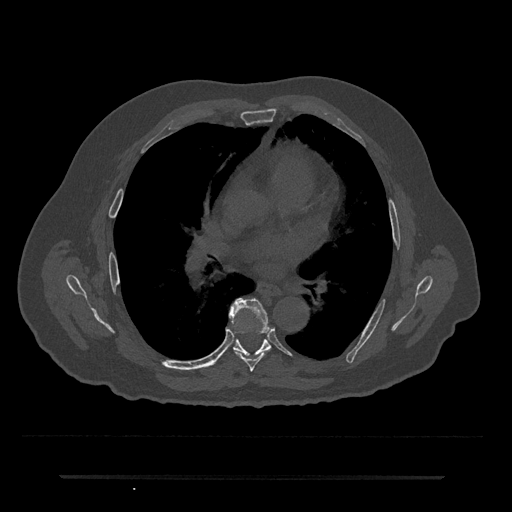
CT including the spine, one axial slice; slice 414 of 797 in the series (ordered by position); reconstruction kernel Br40s/3; 120 kVp; bone window (W 1800 / L 400 HU); 512 × 512 image matrix, field of view 437 × 437 mm. Patient: male, 69 years. From the clinical record (not read from this slice): primary cancer: prostate.
Outlined on this slice (semi-automatically segmented with operator editing):
- T6 vertebra: bounding box (x1, y1, x2, y2) in pixels: (230, 298, 272, 372)
- T7 vertebra: (232, 339, 271, 356)